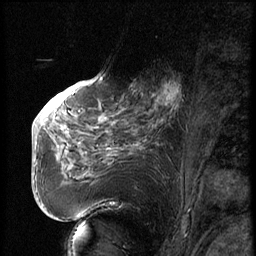
Breast MRI (dynamic contrast-enhanced), one sagittal slice. Dynamic contrast-enhanced series, image 2 of 3 at this slice position (ordered by acquisition). 1.5 T. TE 4.2 ms, TR 9 ms. 2.5 mm slice thickness. 256 × 256 image matrix. Patient: female, 56 years. Case-level facts recorded for this patient, not image findings: setting: breast cancer imaged before/during neoadjuvant chemotherapy.
Structures marked on this image (semi-automatically segmented with operator editing):
- analysis volume of interest (the breast-tissue region the enhancement analysis was run in; not a lesion): bounding box (x1, y1, x2, y2) in pixels: (123, 71, 195, 131)
- tumour enhancement mask (voxels above the 140 % enhancement threshold inside the analysis volume of interest): (153, 81, 182, 109)